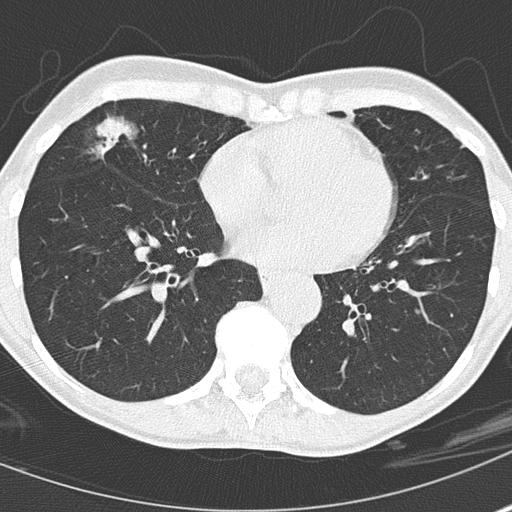
Axial slice from a low-dose chest CT screening exam. Second screening round (one year after baseline). Lung window (W 1500 / L -600 HU). Slice 106 of 167 in the series. Female participant, aged 67 years at enrolment. Current smoker at enrolment.
- Expert-annotated lung lesion, box from (x=83, y=109) to (x=189, y=199) px.
- The screening reader recorded 2 non-calcified nodules or masses ≥4 mm on this exam; which of them this box marks is not recorded.
- Official screen result: positive, other.
- Participant outcome: lung cancer diagnosed 475 days after this screen — bronchiolo-alveolar adenocarcinoma, NOS, right middle lobe, well differentiated (G1), stage IA (AJCC 6th edition), 25 mm at pathology.